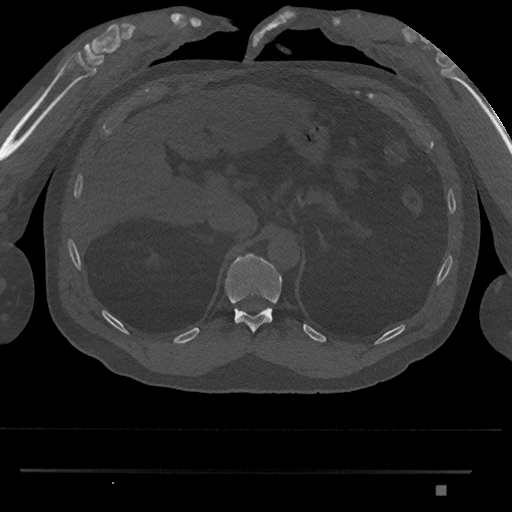
CT including the spine, one axial slice; slice 941 of 1134 in the series (ordered by position); bone window (W 1800 / L 400 HU); 512 × 512 image matrix. Patient: male, 65 years. Case-level facts recorded for this patient, not image findings: primary cancer: prostate.
Outlined on this slice (semi-automatic segmentation, software-assisted and operator-edited):
- T11 vertebra: bounding box [x1, y1, x2, y2] px = [225, 253, 283, 333]